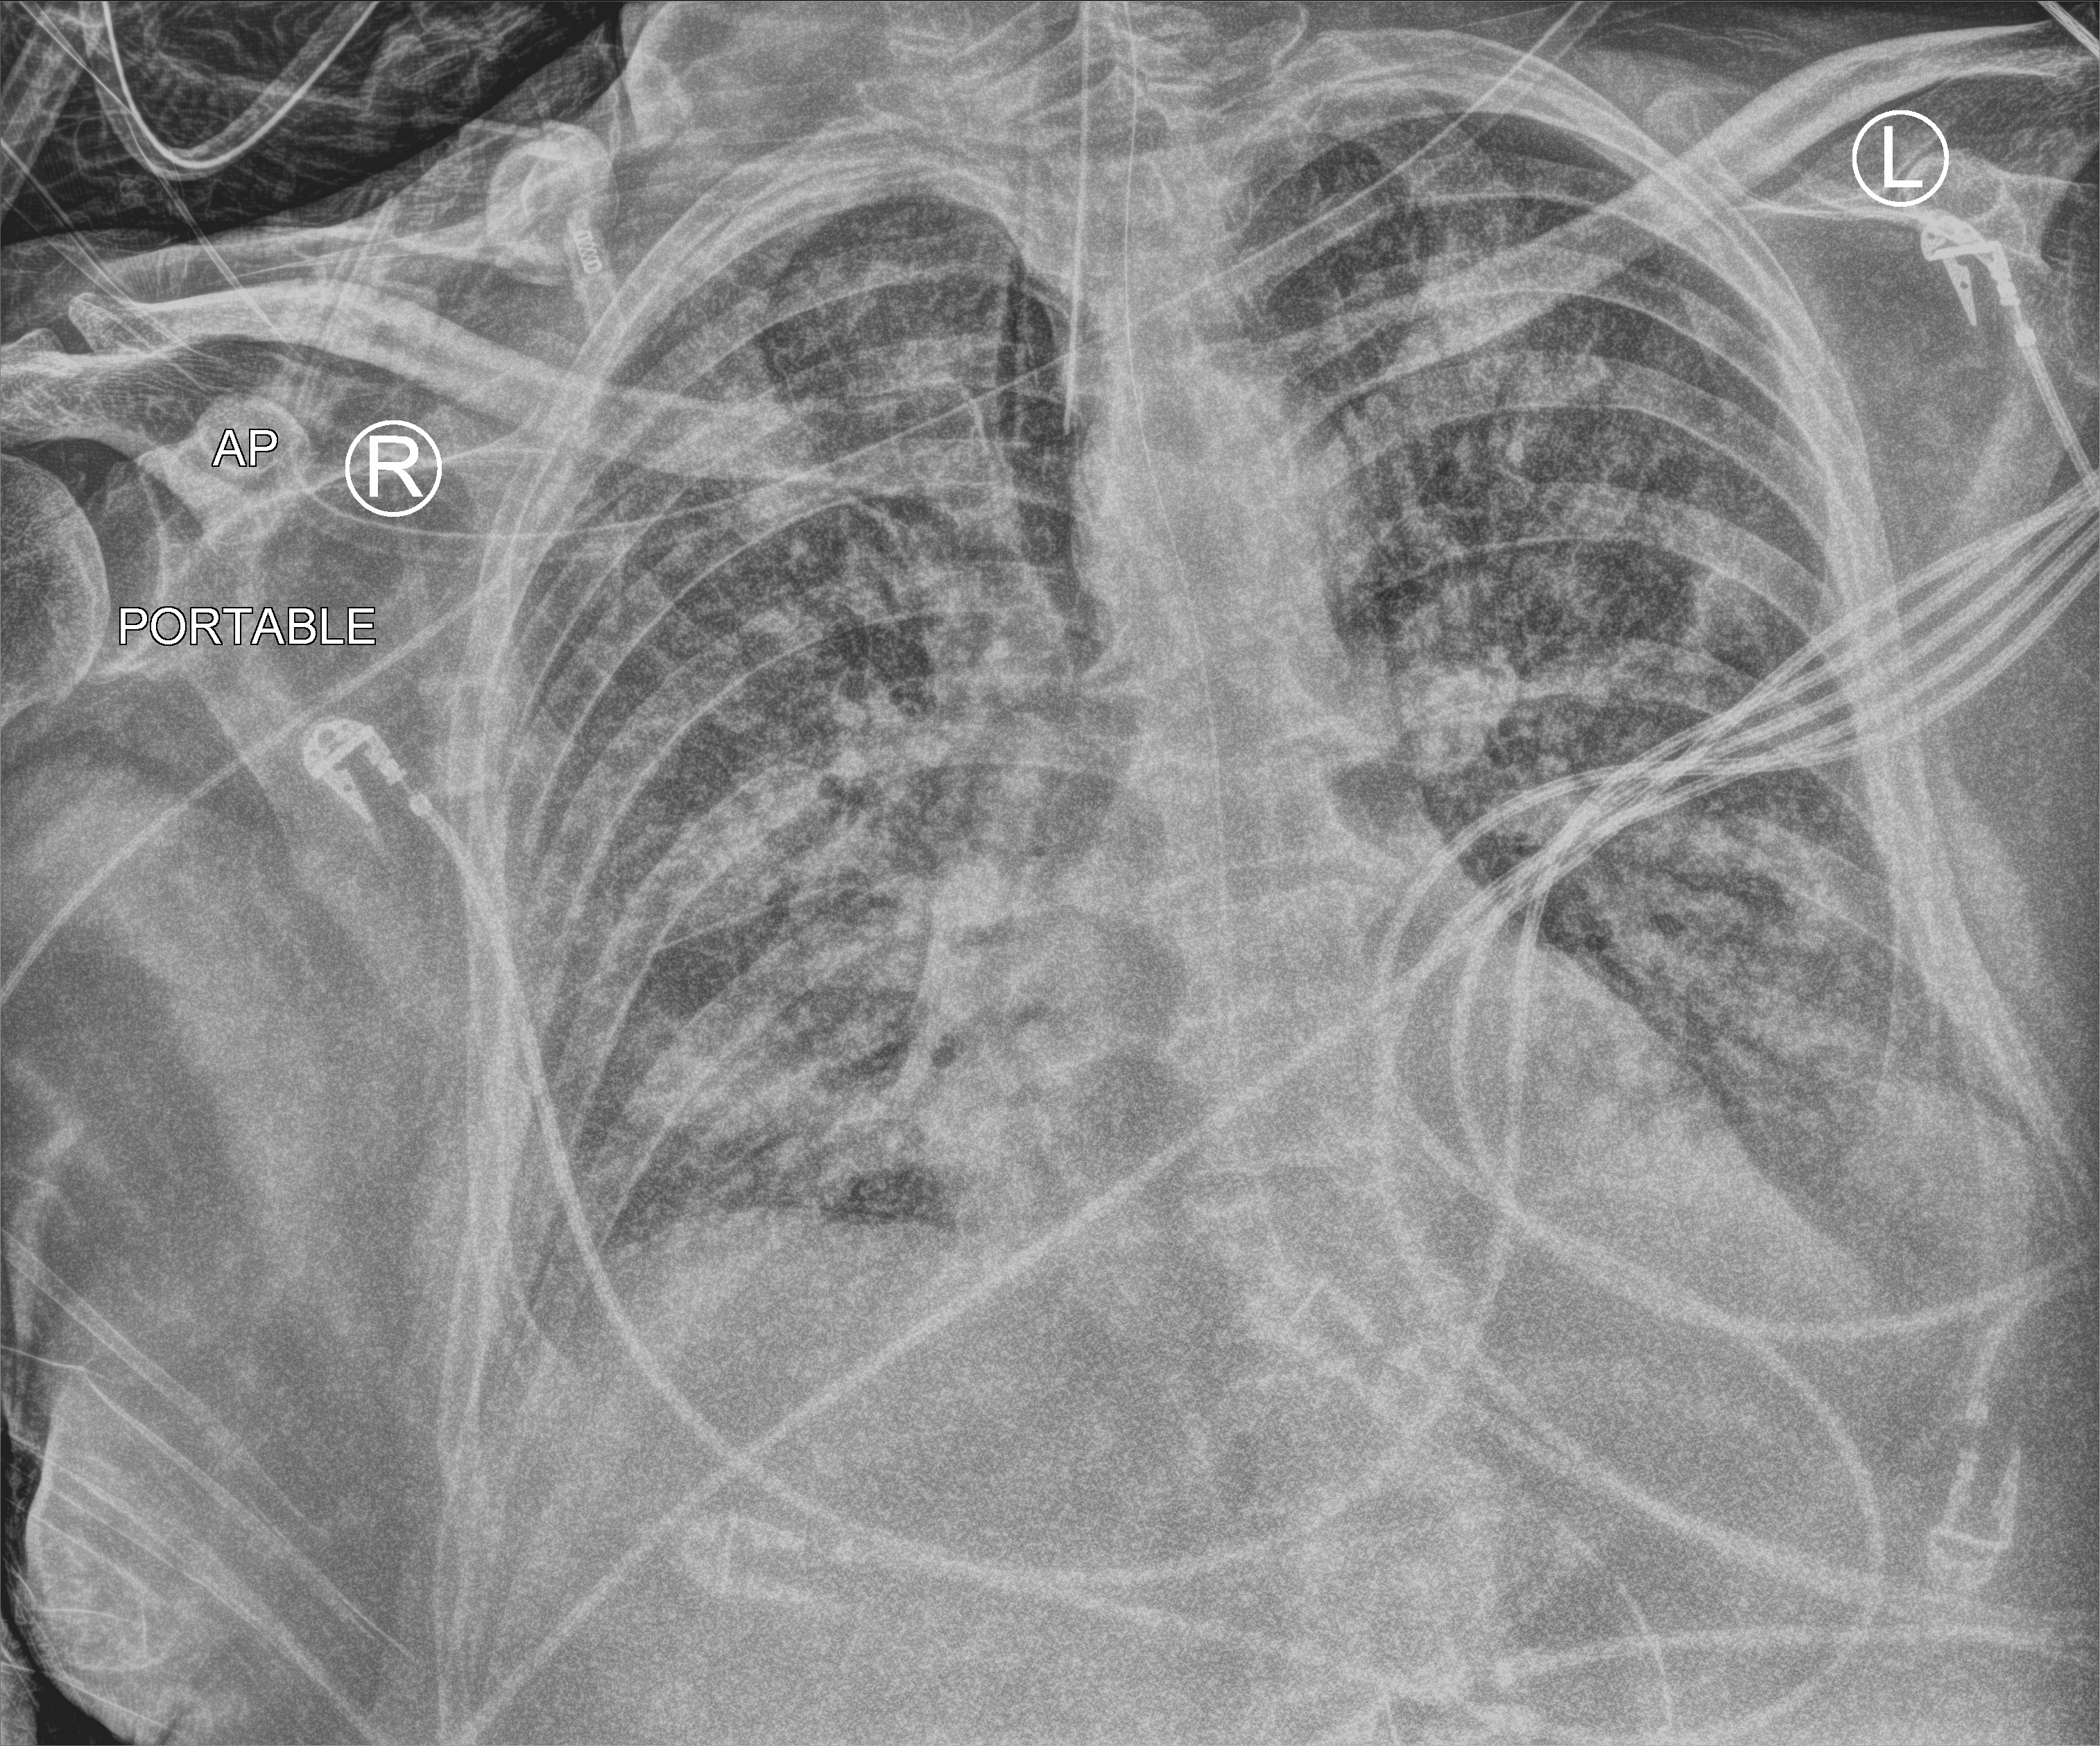
Bedside chest radiograph (computed radiography); anteroposterior (AP) projection. Patient hospitalised with COVID-19; male, aged 60–74 years.
Admission-level facts for this patient (not findings on this image; timing relative to this image not recorded): mechanically ventilated during this hospital stay: yes; hypertension (admission record): yes; admitted to intensive care during this hospital stay: yes.